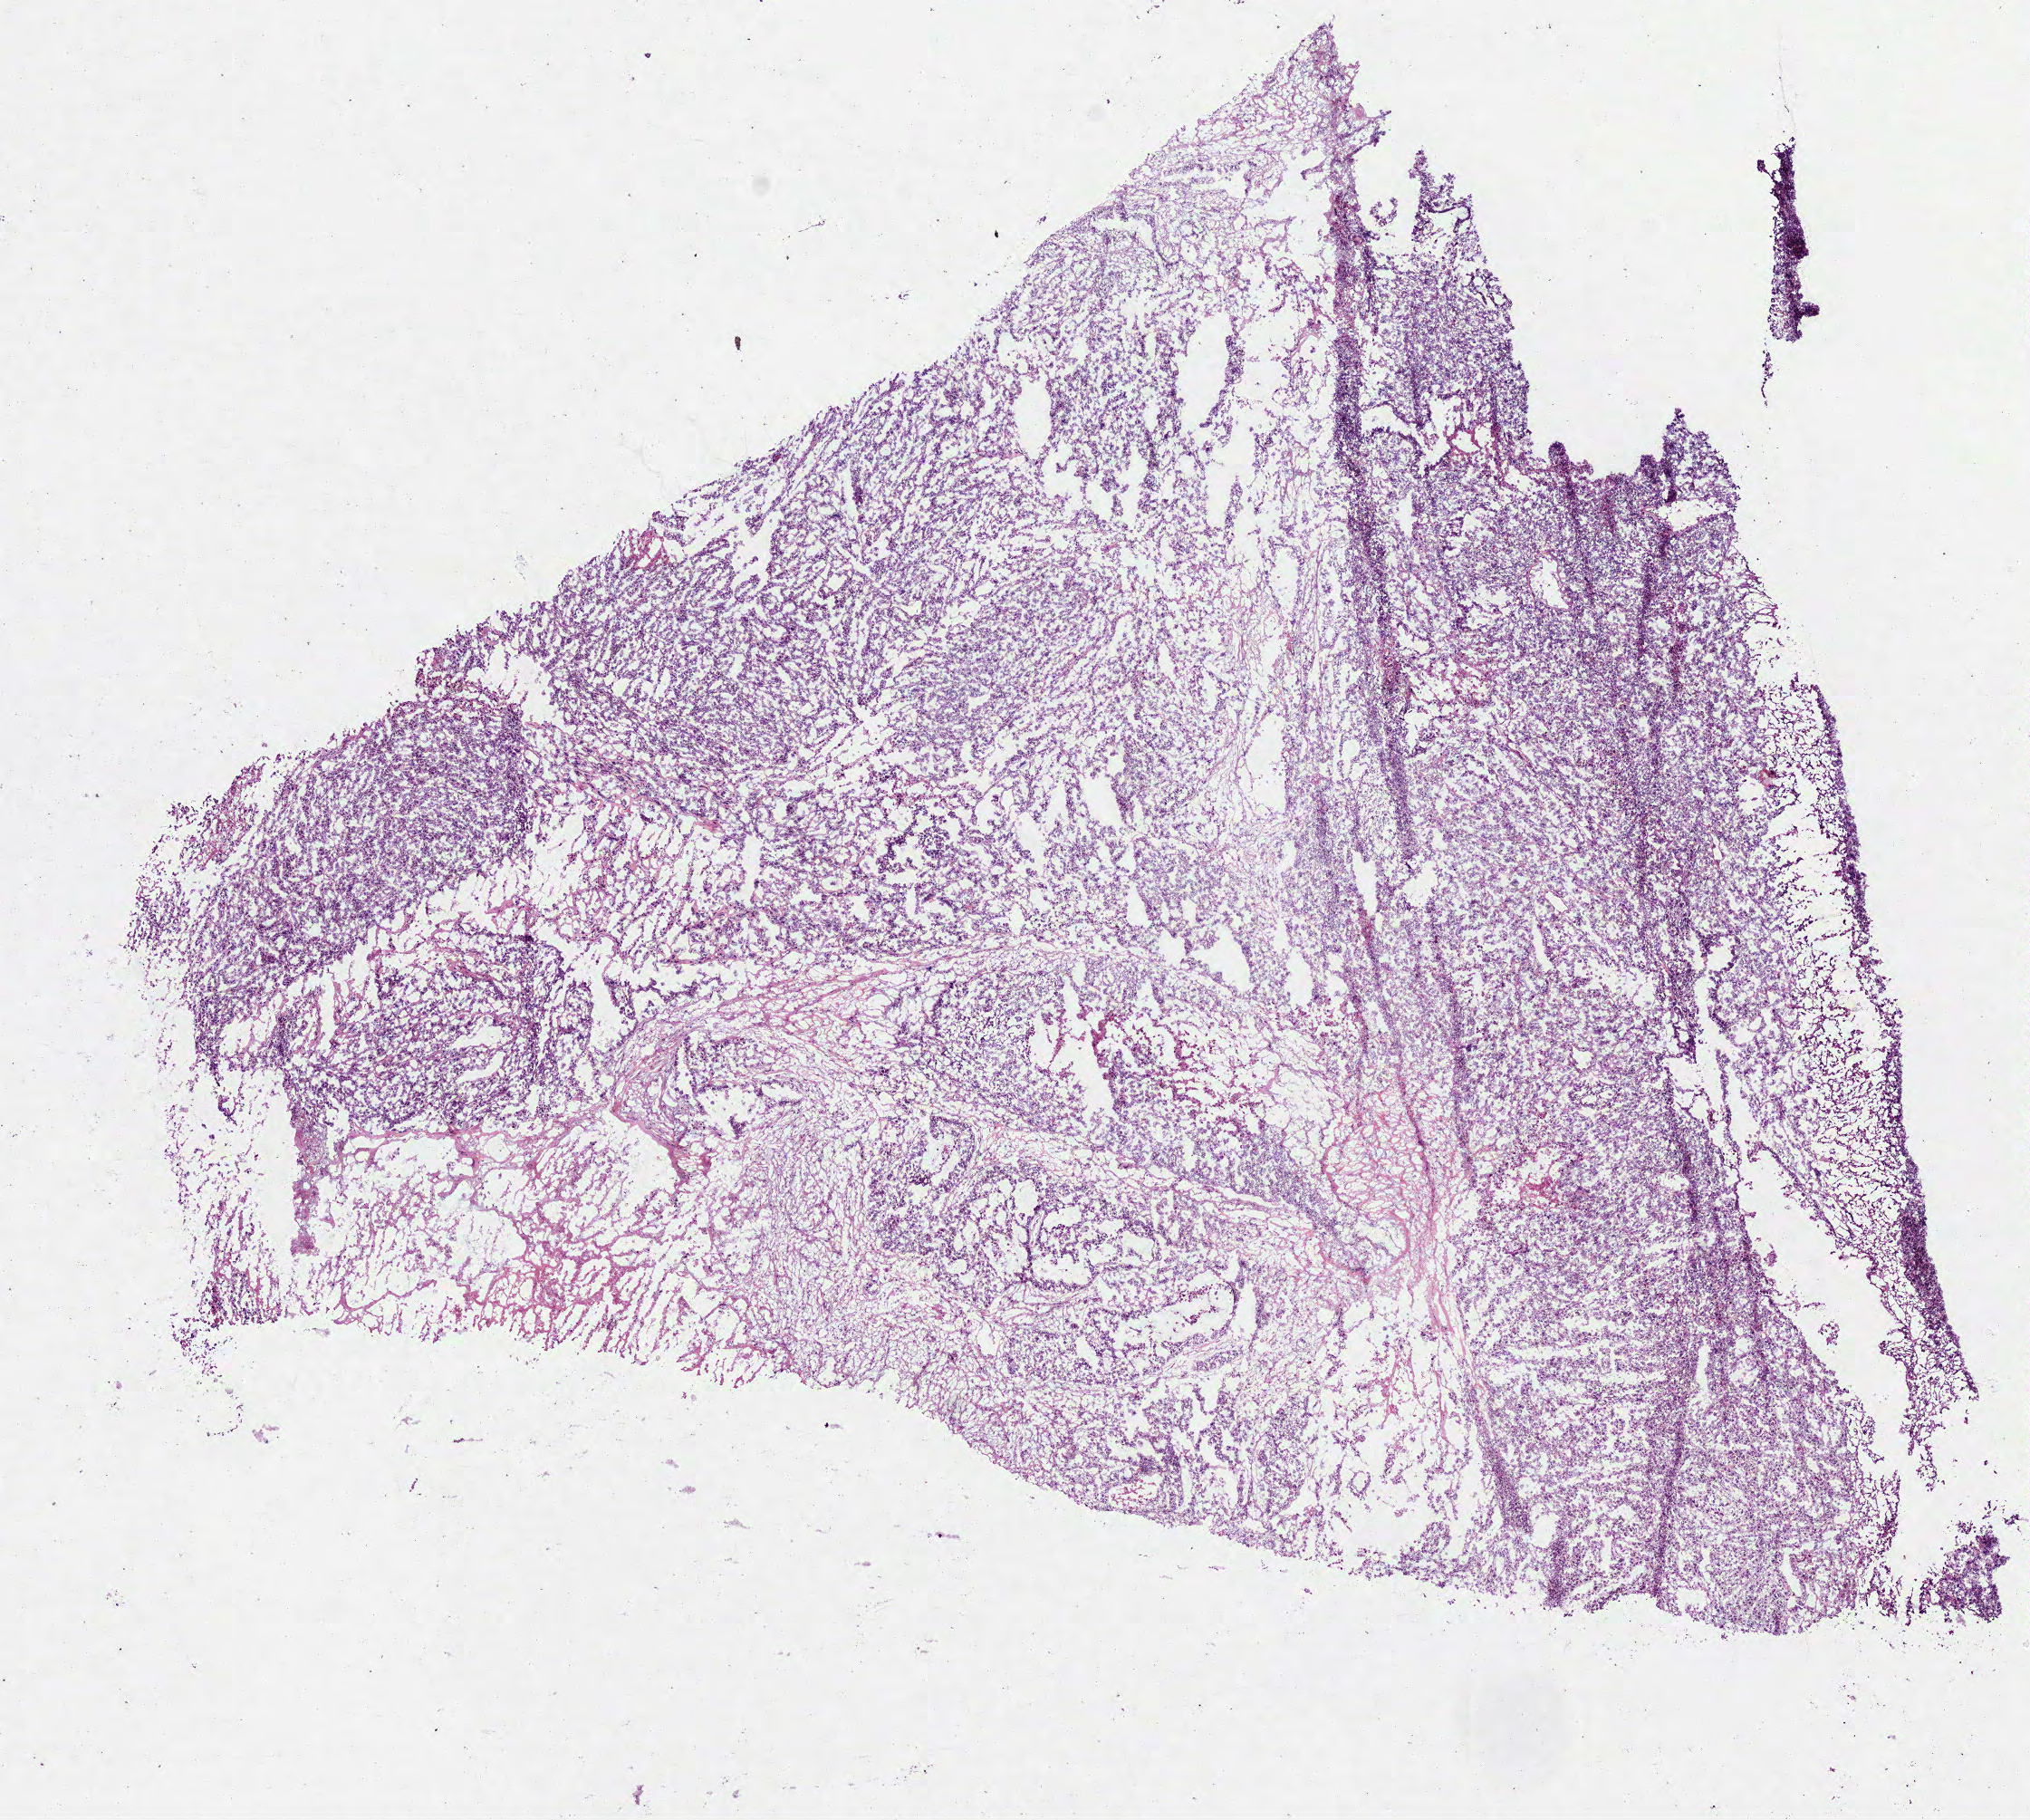
Digitized Hematoxylin and eosin (H&E) stained tissue section (whole slide) — whole scanned area (about 9.0 x 8.1 mm) shown as a low-resolution overview, frozen section from the bottom of the tissue portion, primary tumour sample from the lung. Patient: female, age at initial diagnosis 63 years. Pathologist review of this section (percent, as recorded): tumour cells 80%, tumour nuclei 85%.
Pathologic diagnosis: Adenocarcinoma, NOS (lower lobe, lung).